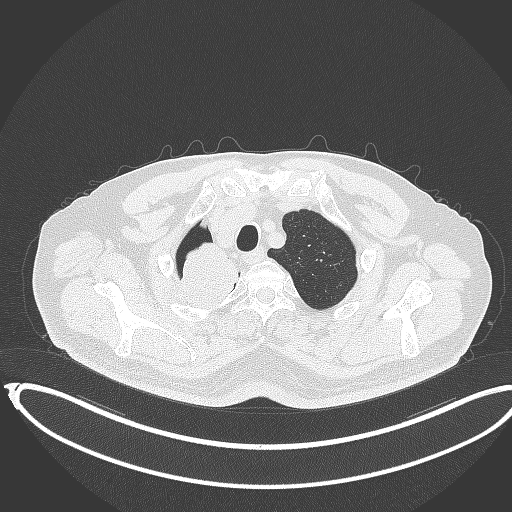
Chest CT, one axial slice. Reconstruction kernel B70f. Lung window (W 1500 / L -600 HU). 1 mm slice thickness. 512 × 512 image matrix, field of view 436 × 436 mm. Patient: male, 68 years. Case-level facts recorded for this patient, not image findings: clinical TNM (as recorded): T2a N0 M0.
Structures marked on this image (rectangle marked by the reading radiologist):
- lung tumour (recorded histology: adenocarcinoma): bounding box (x1, y1, x2, y2) in pixels: (176, 240, 239, 306)